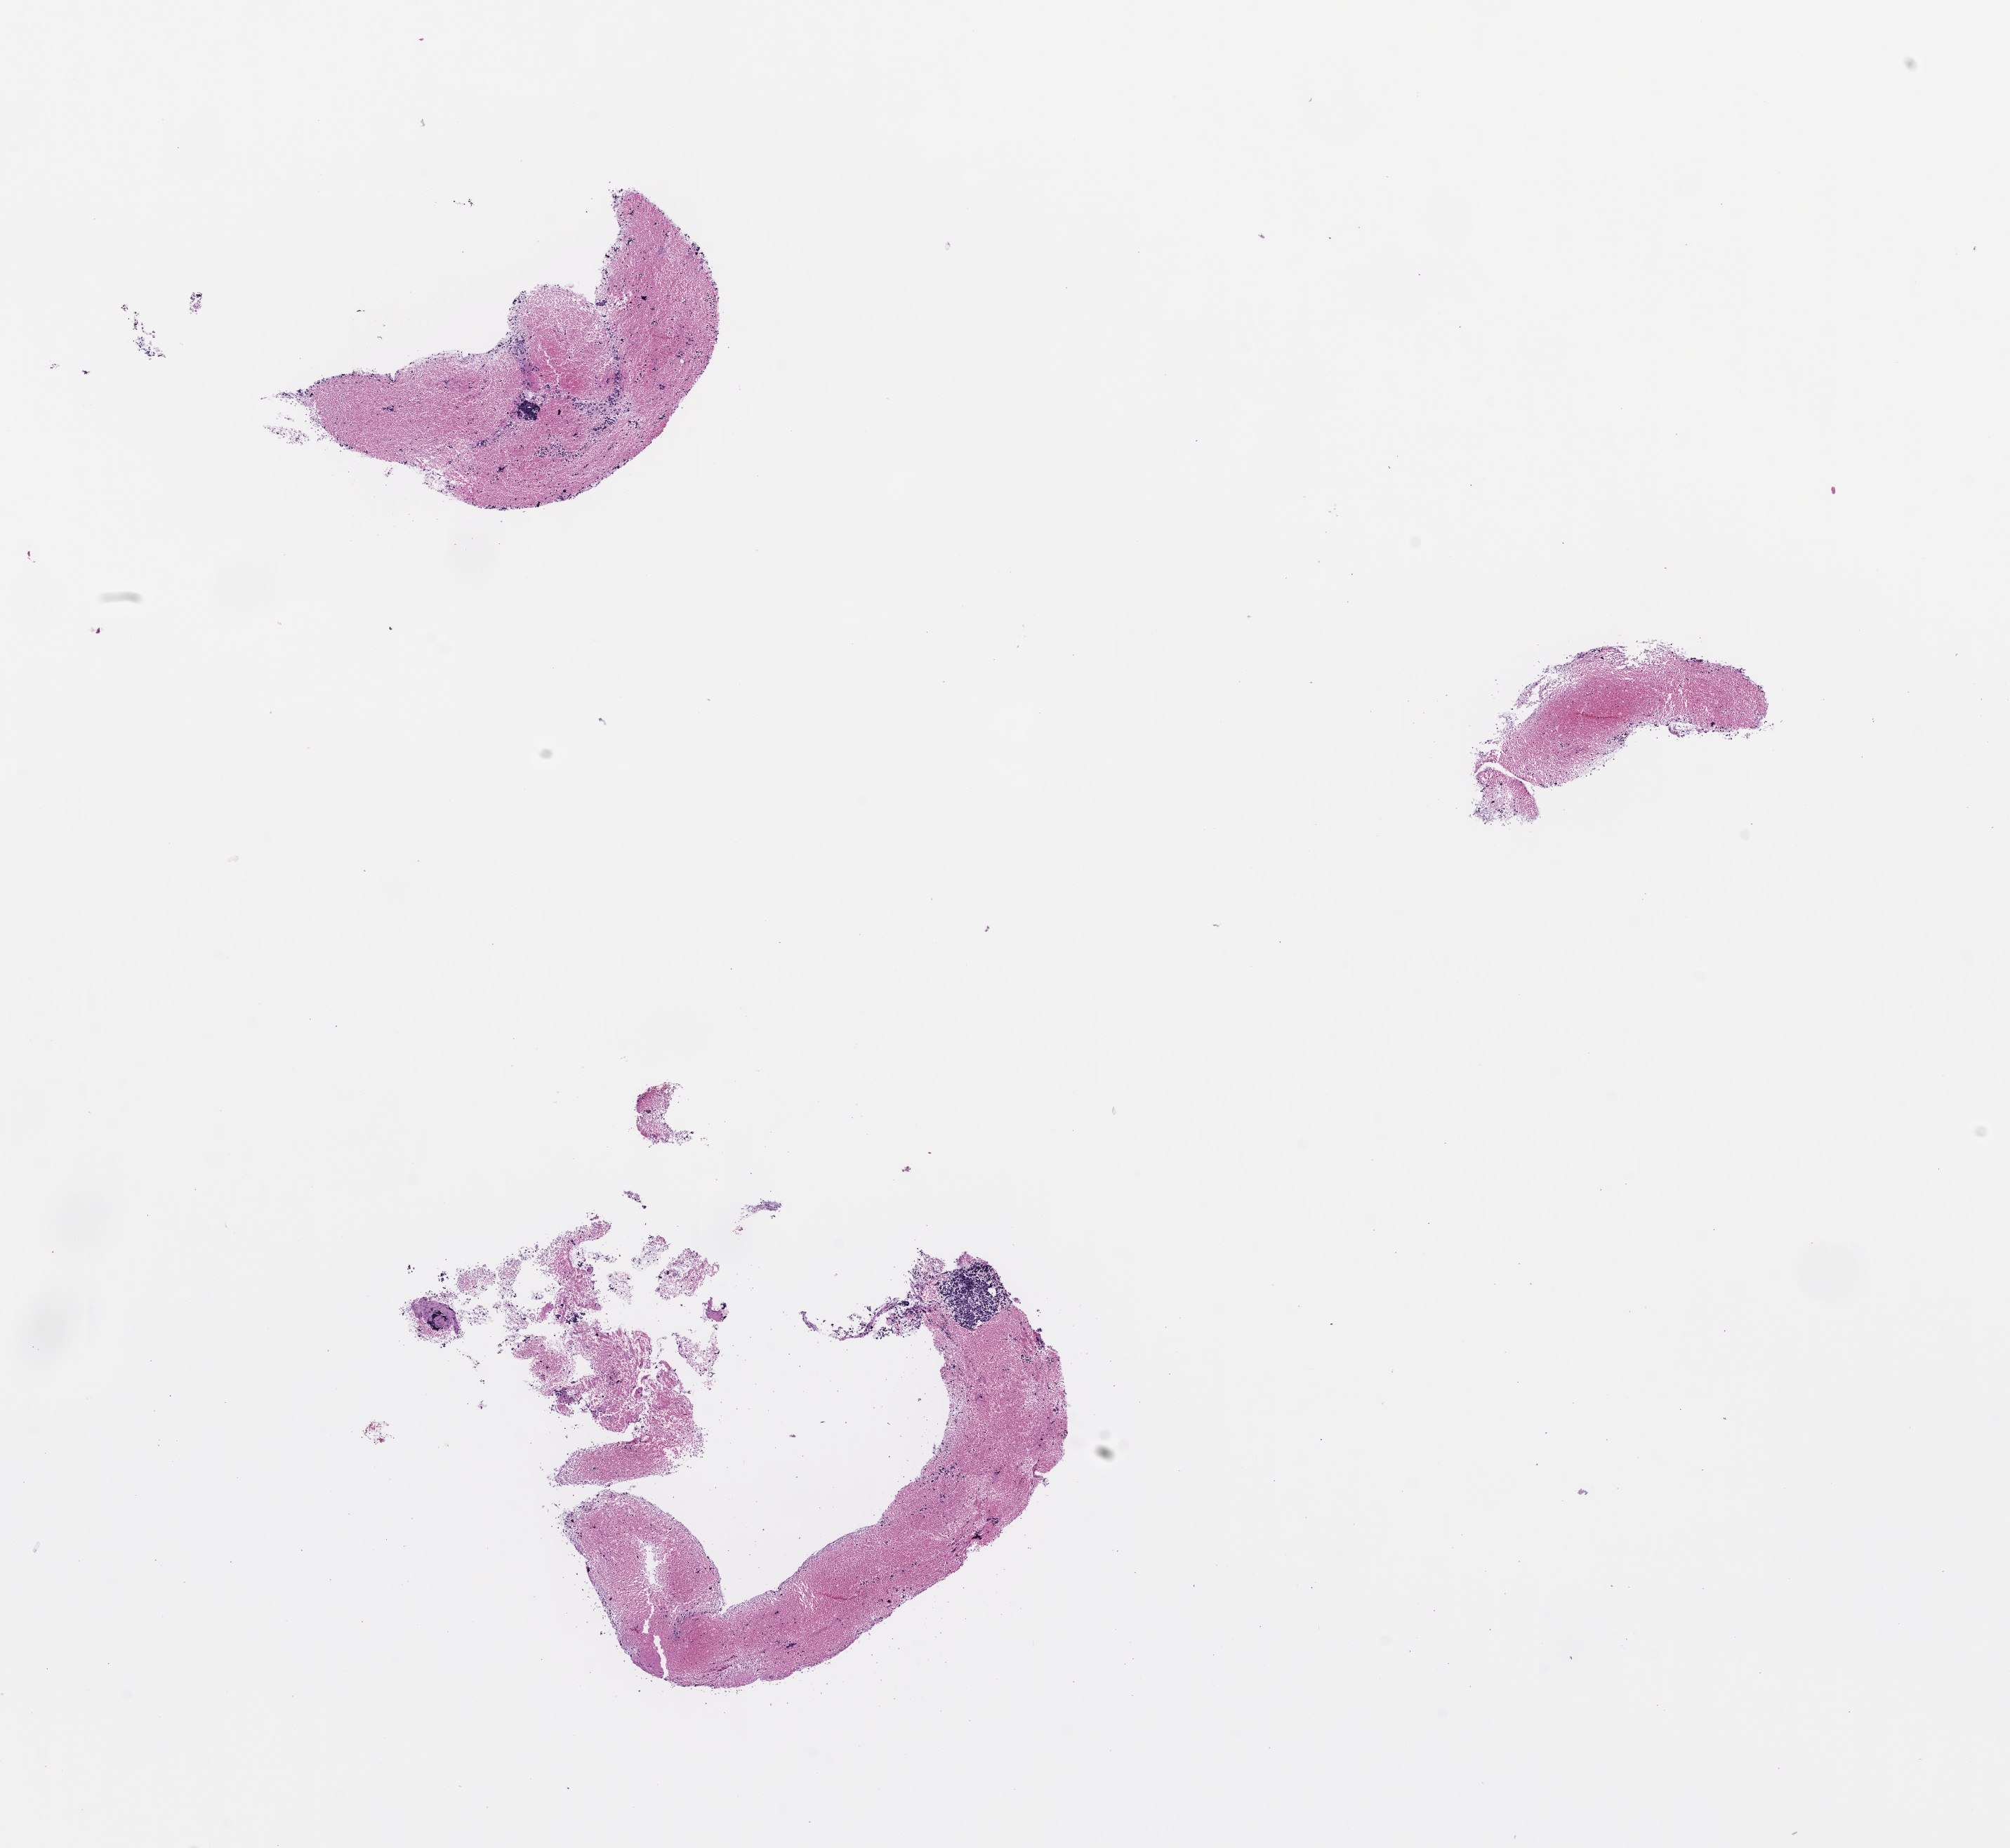
H&E whole-slide image — low-resolution overview of the scanned area, about 11.6 x 10.6 mm, FFPE section, specimen time point: collected at baseline (before treatment). Patient: male.
This section: metastasis (sampled organ not recorded). Primary diagnosis of the patient: Small Cell Lung Carcinoma.